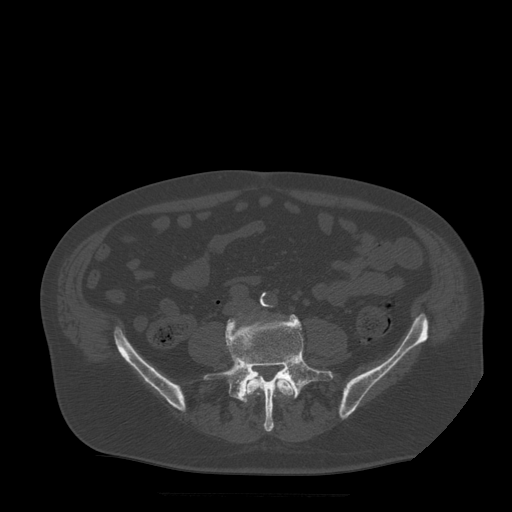
CT including the spine, one axial slice. Slice 96 of 522 in the series (ordered by position). Bone window (W 1800 / L 400 HU). 512 × 512 image matrix, field of view 420 × 420 mm. Patient age 72 years. Case-level facts recorded for this patient, not image findings: primary cancer: prostate.
Structures marked on this image (semi-automatically segmented with operator editing):
- L4 vertebra: bounding box <242,377,296,403> (left, top, right, bottom; pixels)
- L5 vertebra: <205,315,335,432>